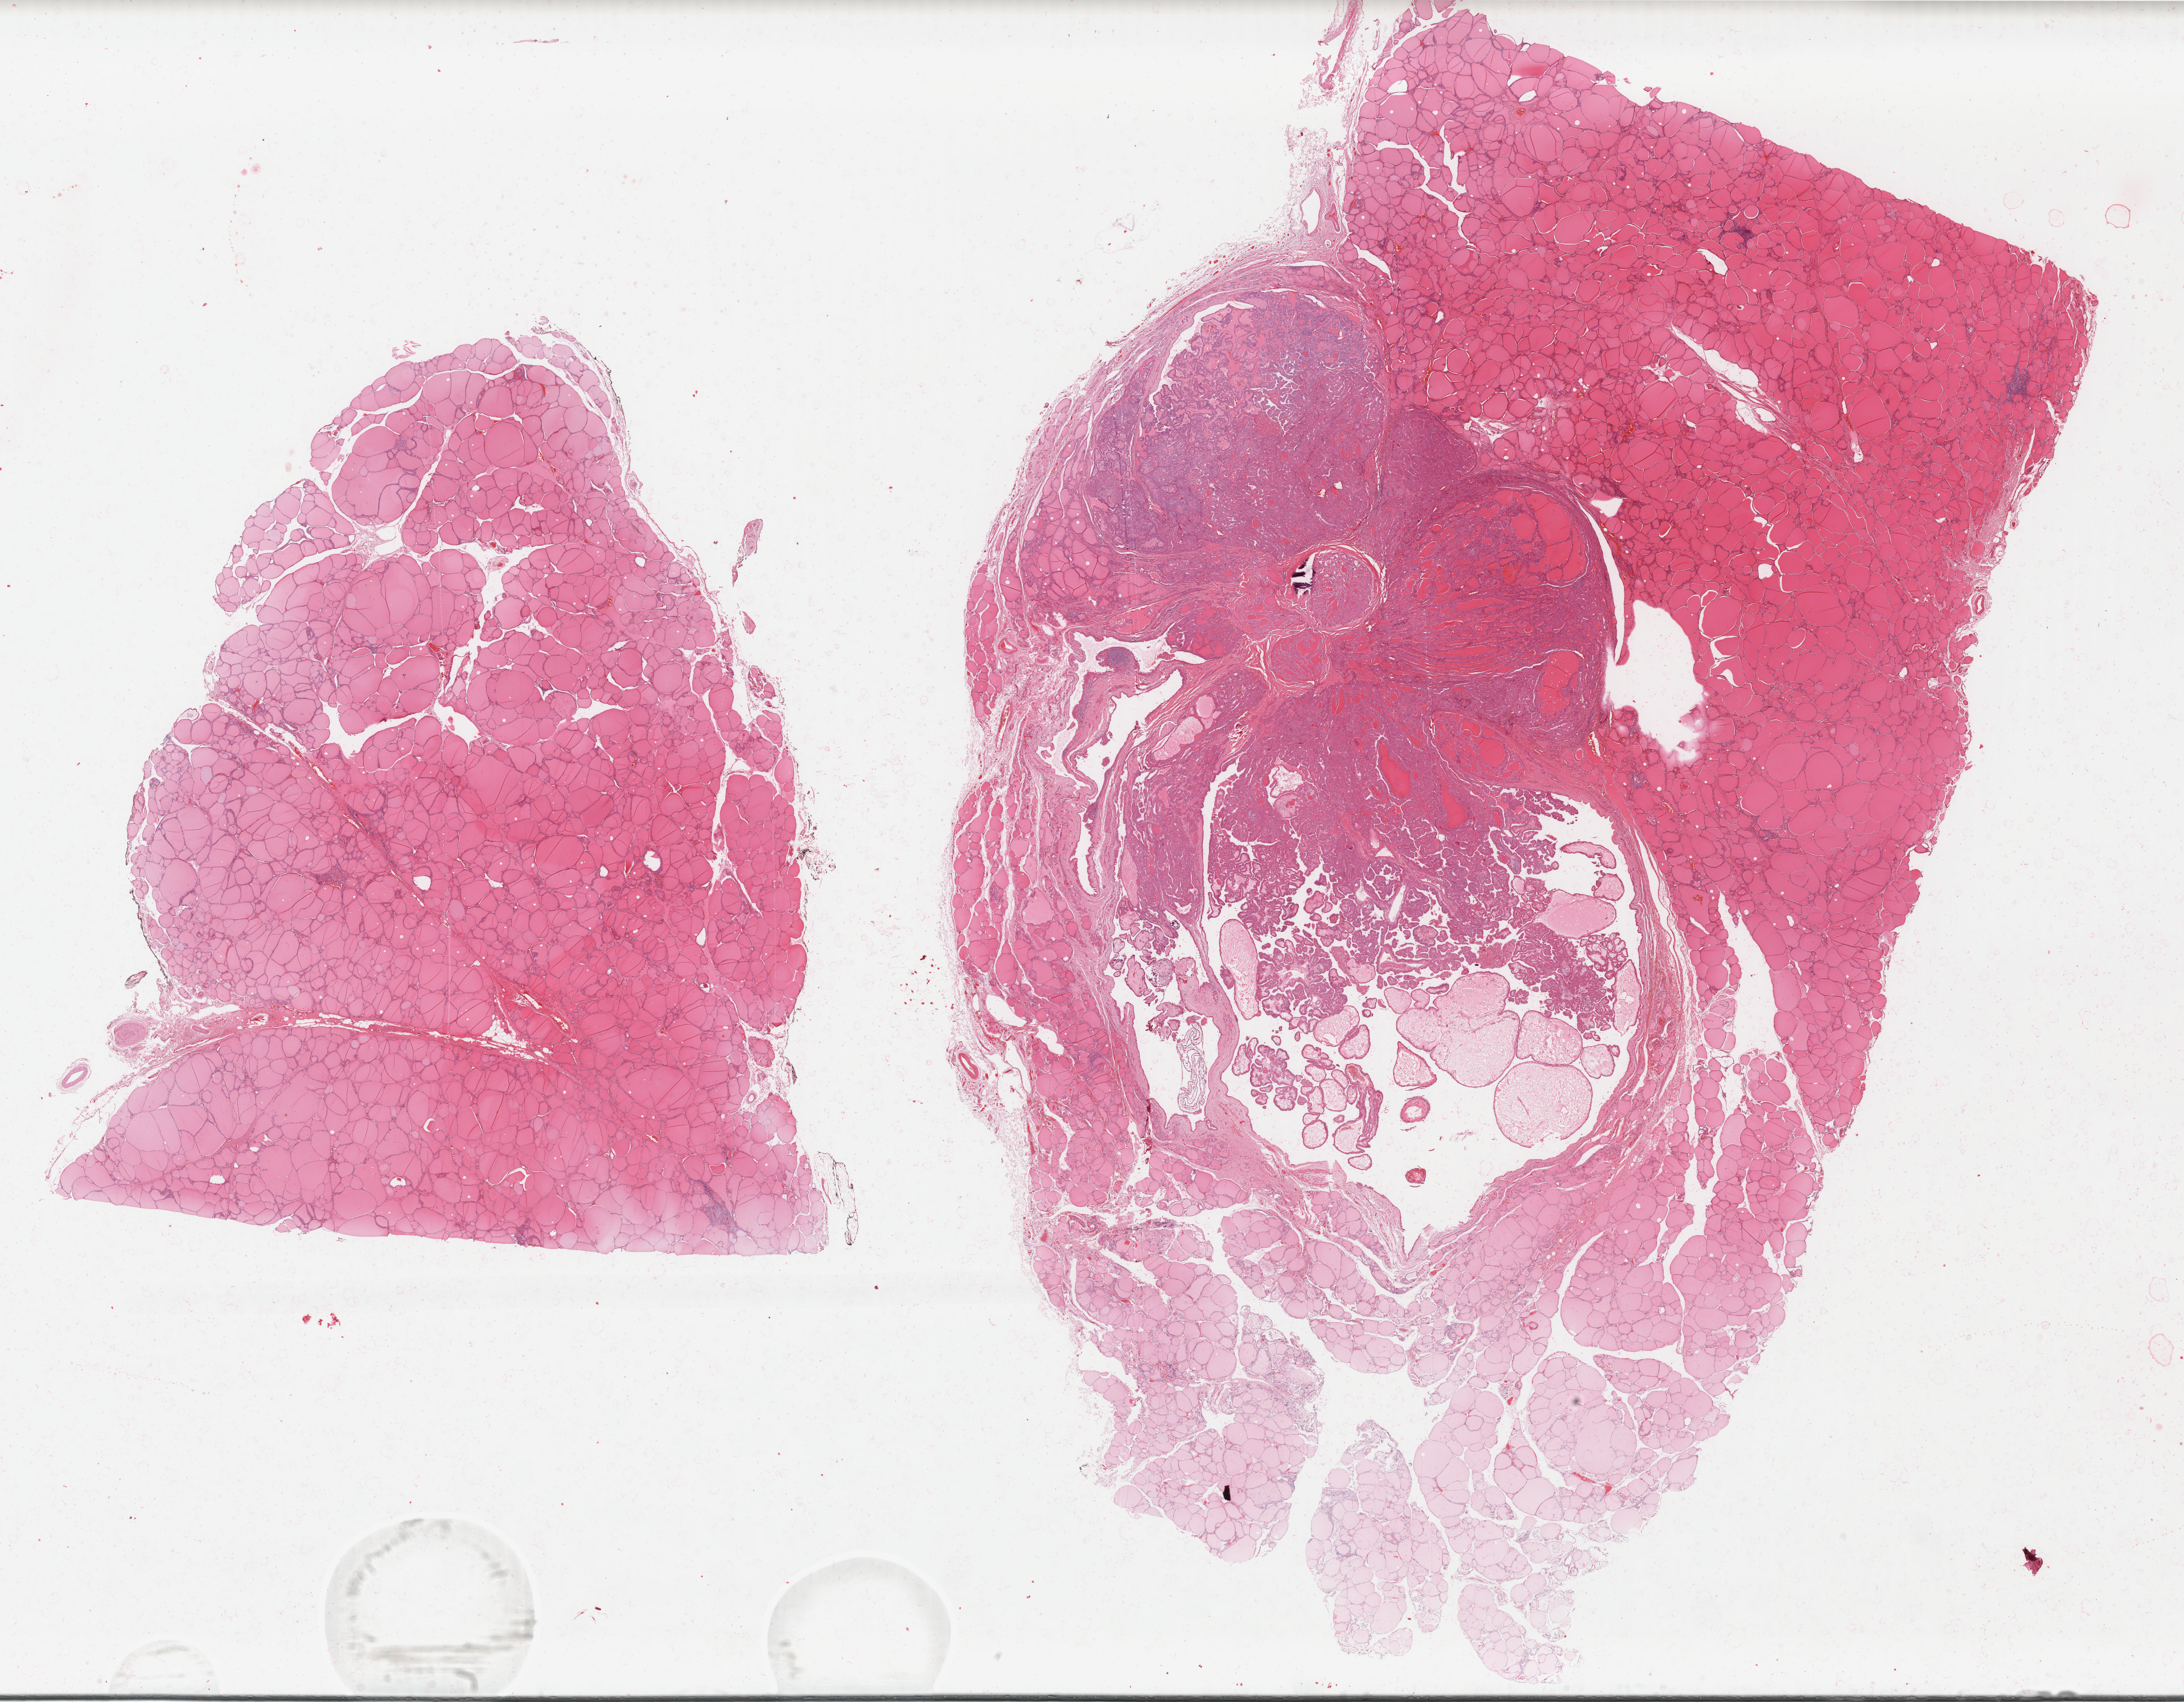
H&E-stained whole-slide image — whole scanned area (about 30.5 x 23.7 mm, from a 40x scan) shown as a low-resolution overview, FFPE section, sample: primary tumour, thyroid. Patient: female, age at initial diagnosis 46 years.
Lymph nodes positive (case pathology): 0 of 2 examined. AJCC pathologic stage: I (6th edition). TNM: T1 N0 M0. Pathologic diagnosis: Papillary adenocarcinoma, NOS (thyroid gland). Laterality: right.